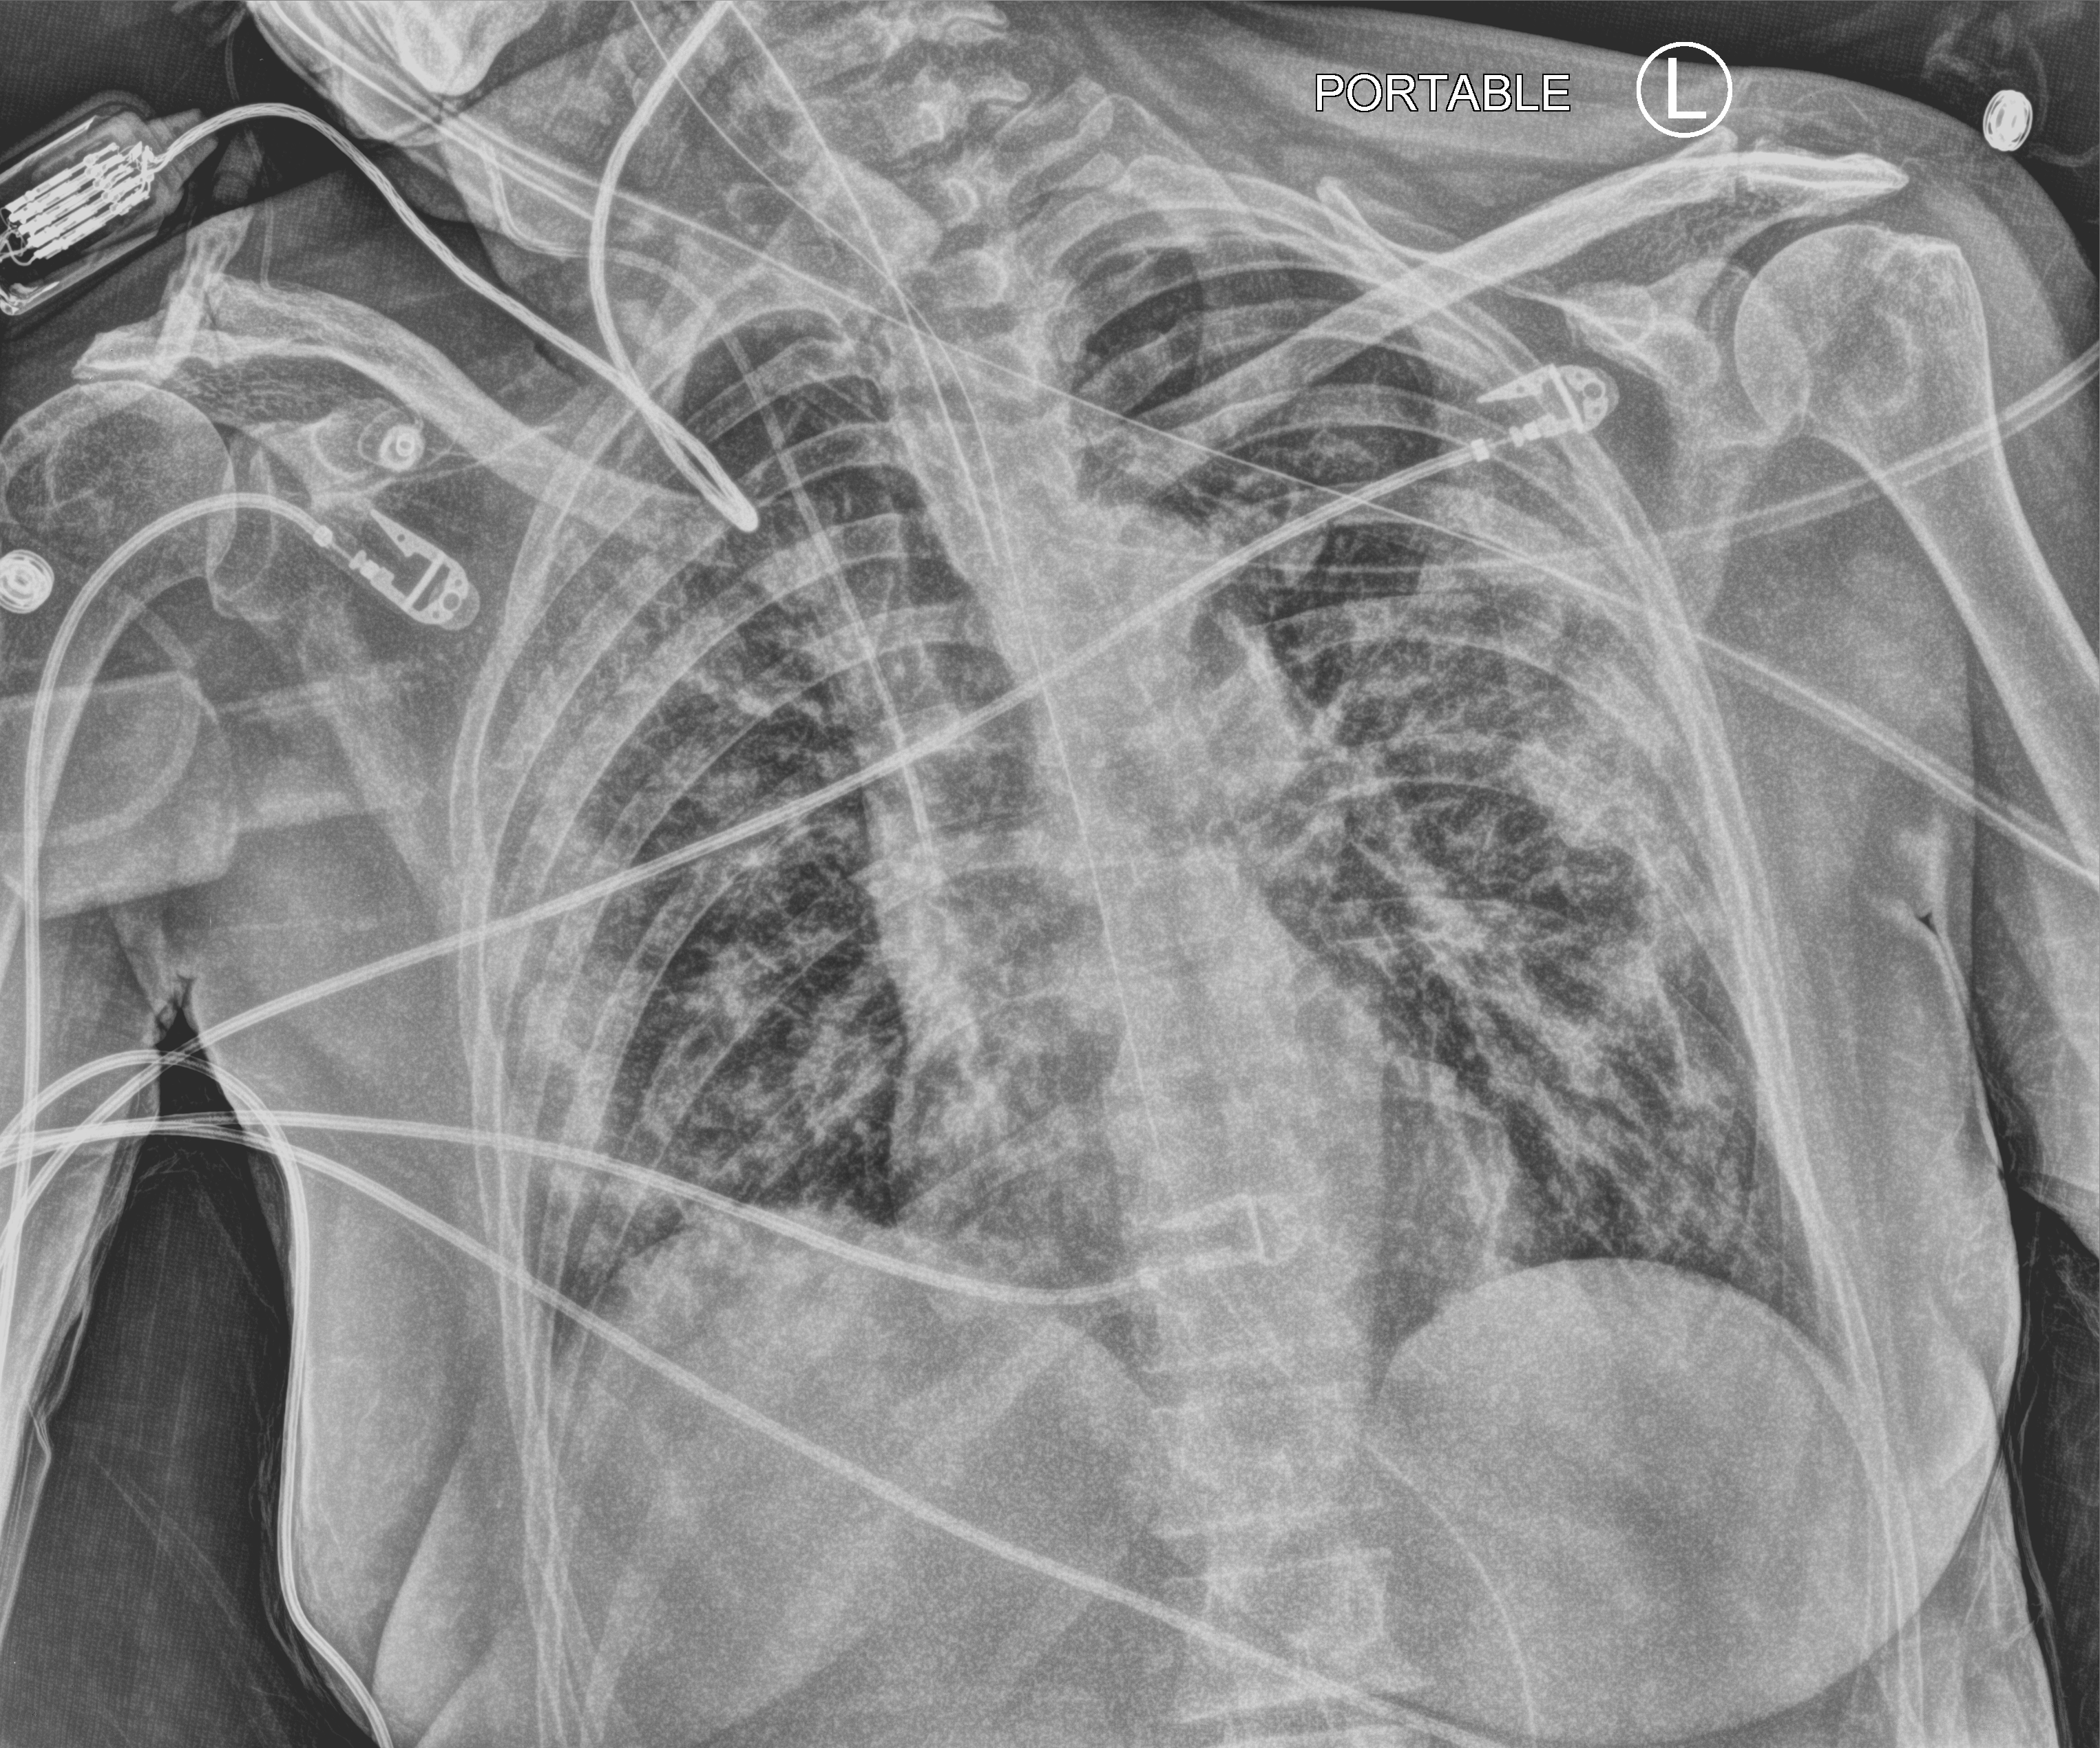
Portable chest radiograph; anteroposterior (AP) projection. Female patient hospitalised with COVID-19, age 60–74 years.
Hospital-stay facts (about this admission, not read from this image; timing relative to this image not recorded):
- admitted to intensive care during this hospital stay: yes
- smoking status (admission record): former